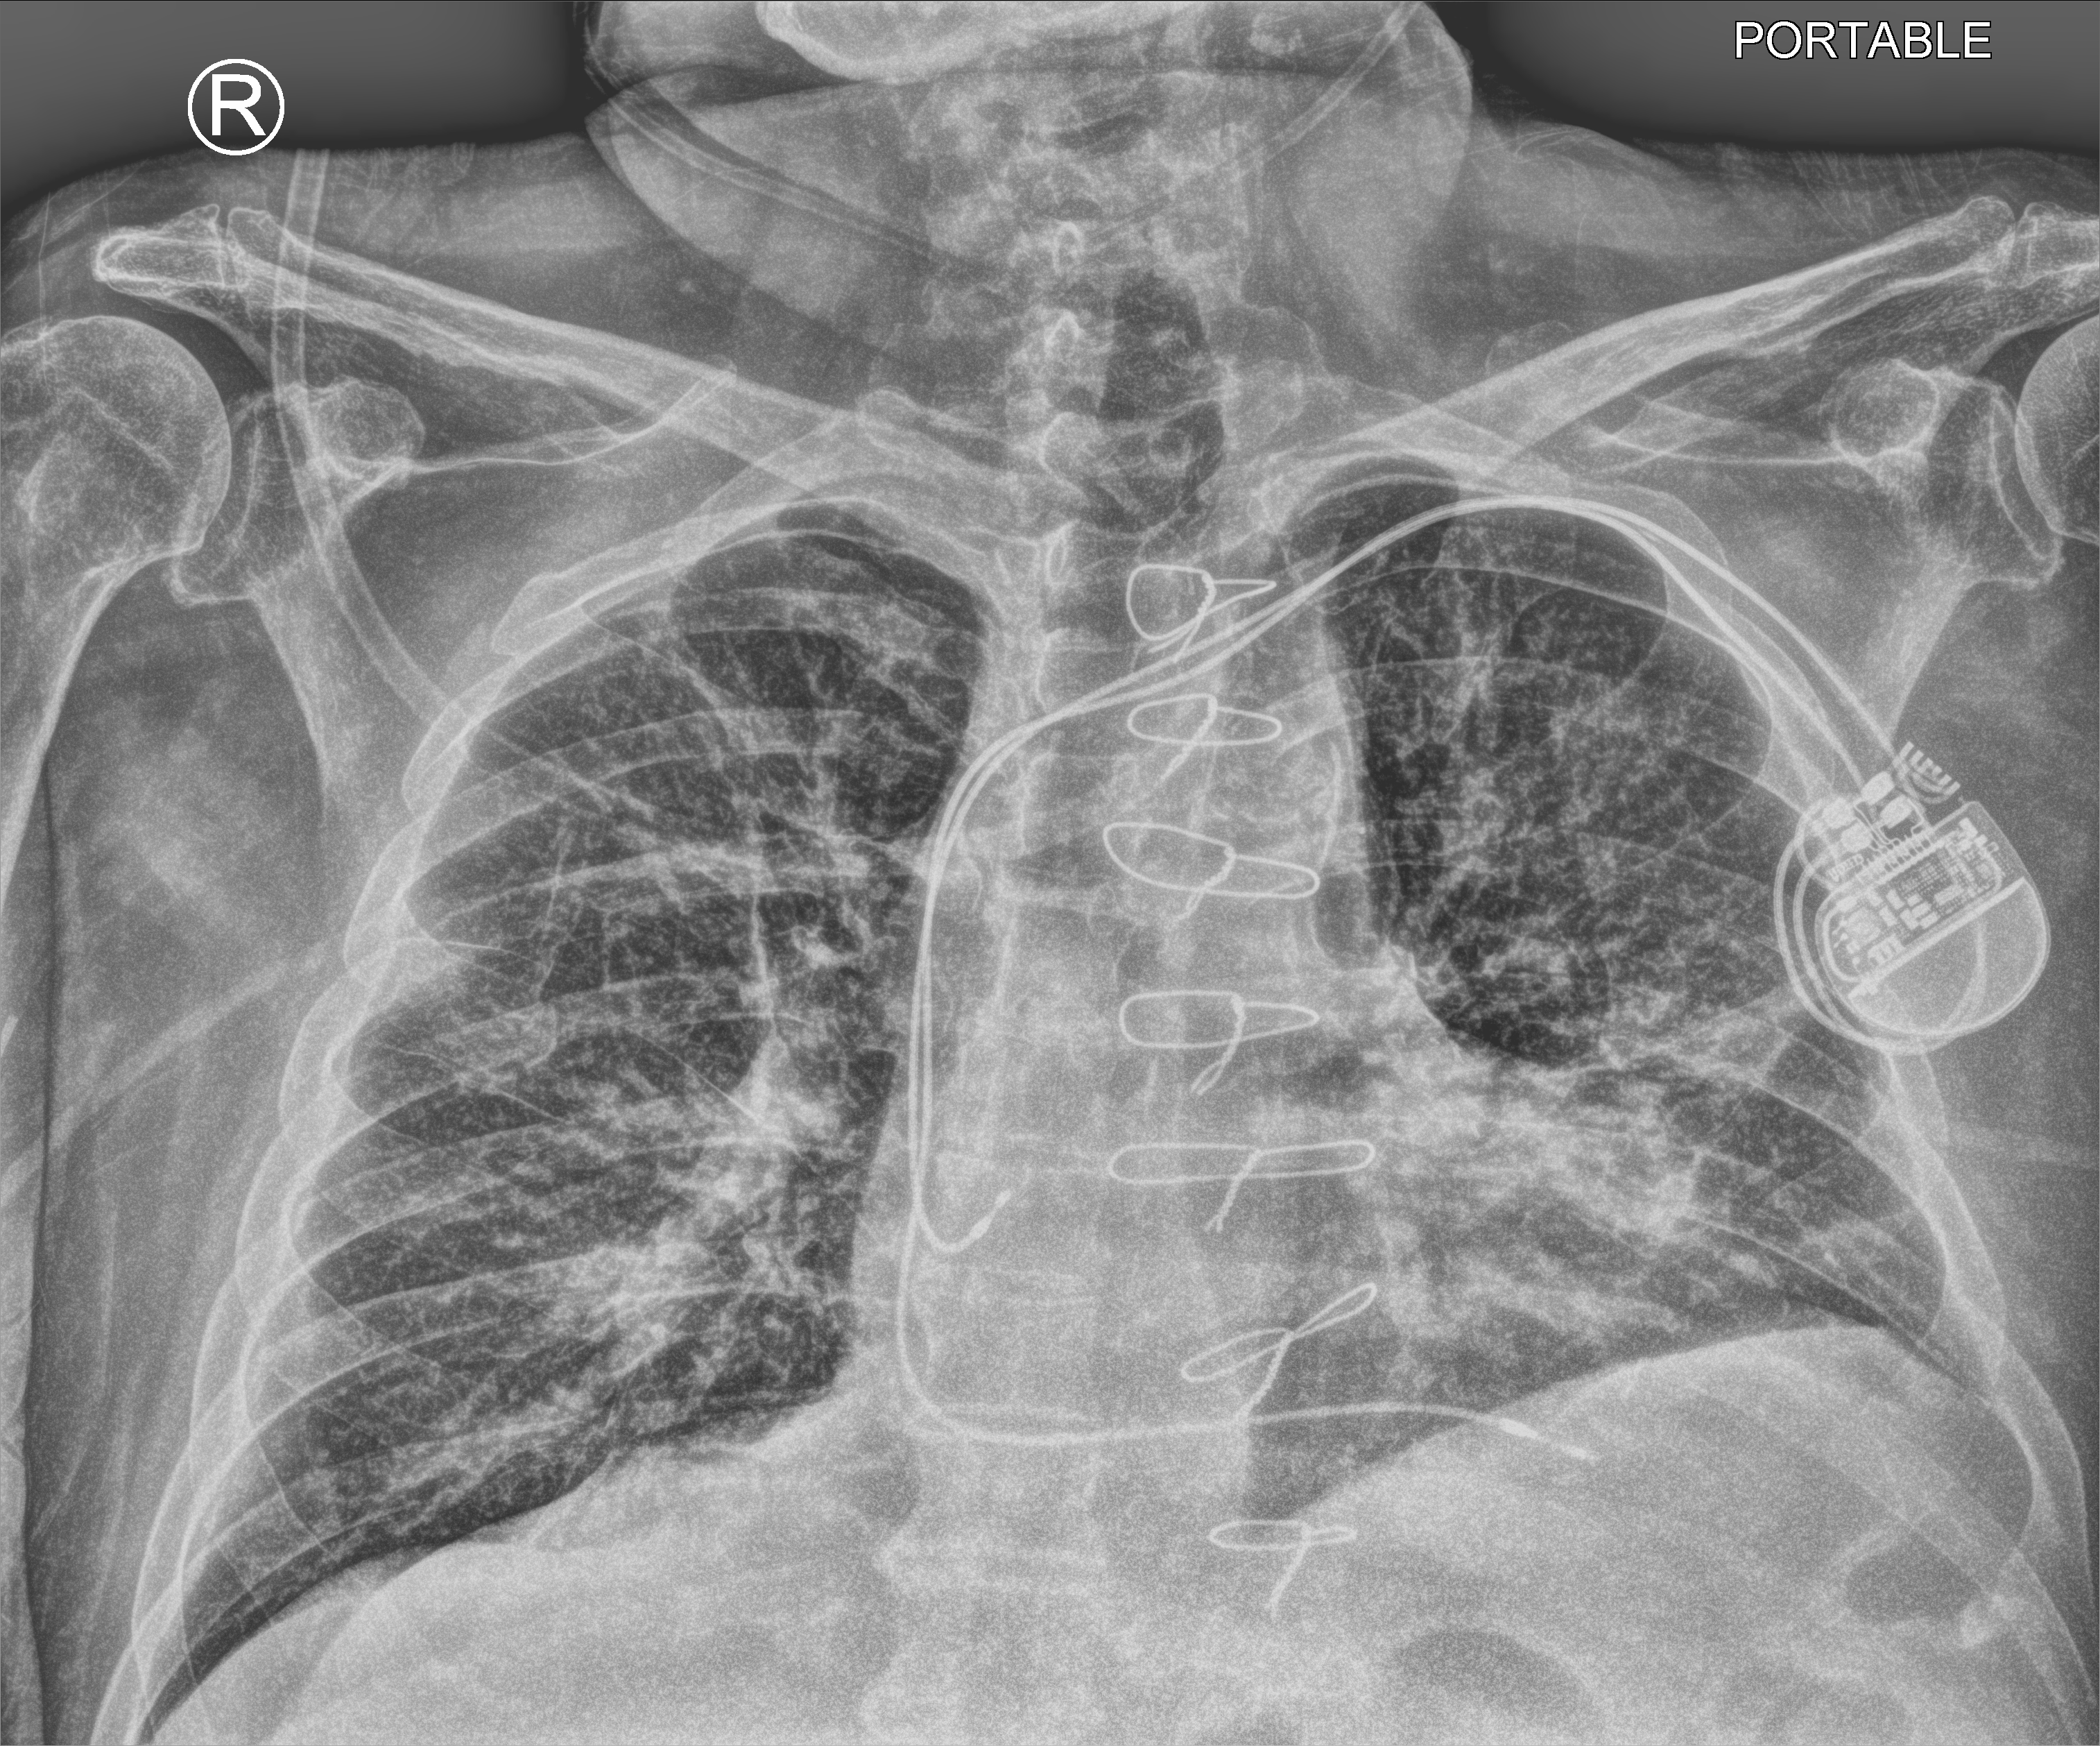
Chest X-ray (portable), anteroposterior (AP) projection. Patient hospitalised with COVID-19; male, aged 75–90 years.
Admission-level facts for this patient (not findings on this image; timing relative to this image not recorded):
- length of hospital stay: 6 days
- mechanically ventilated during this hospital stay: no